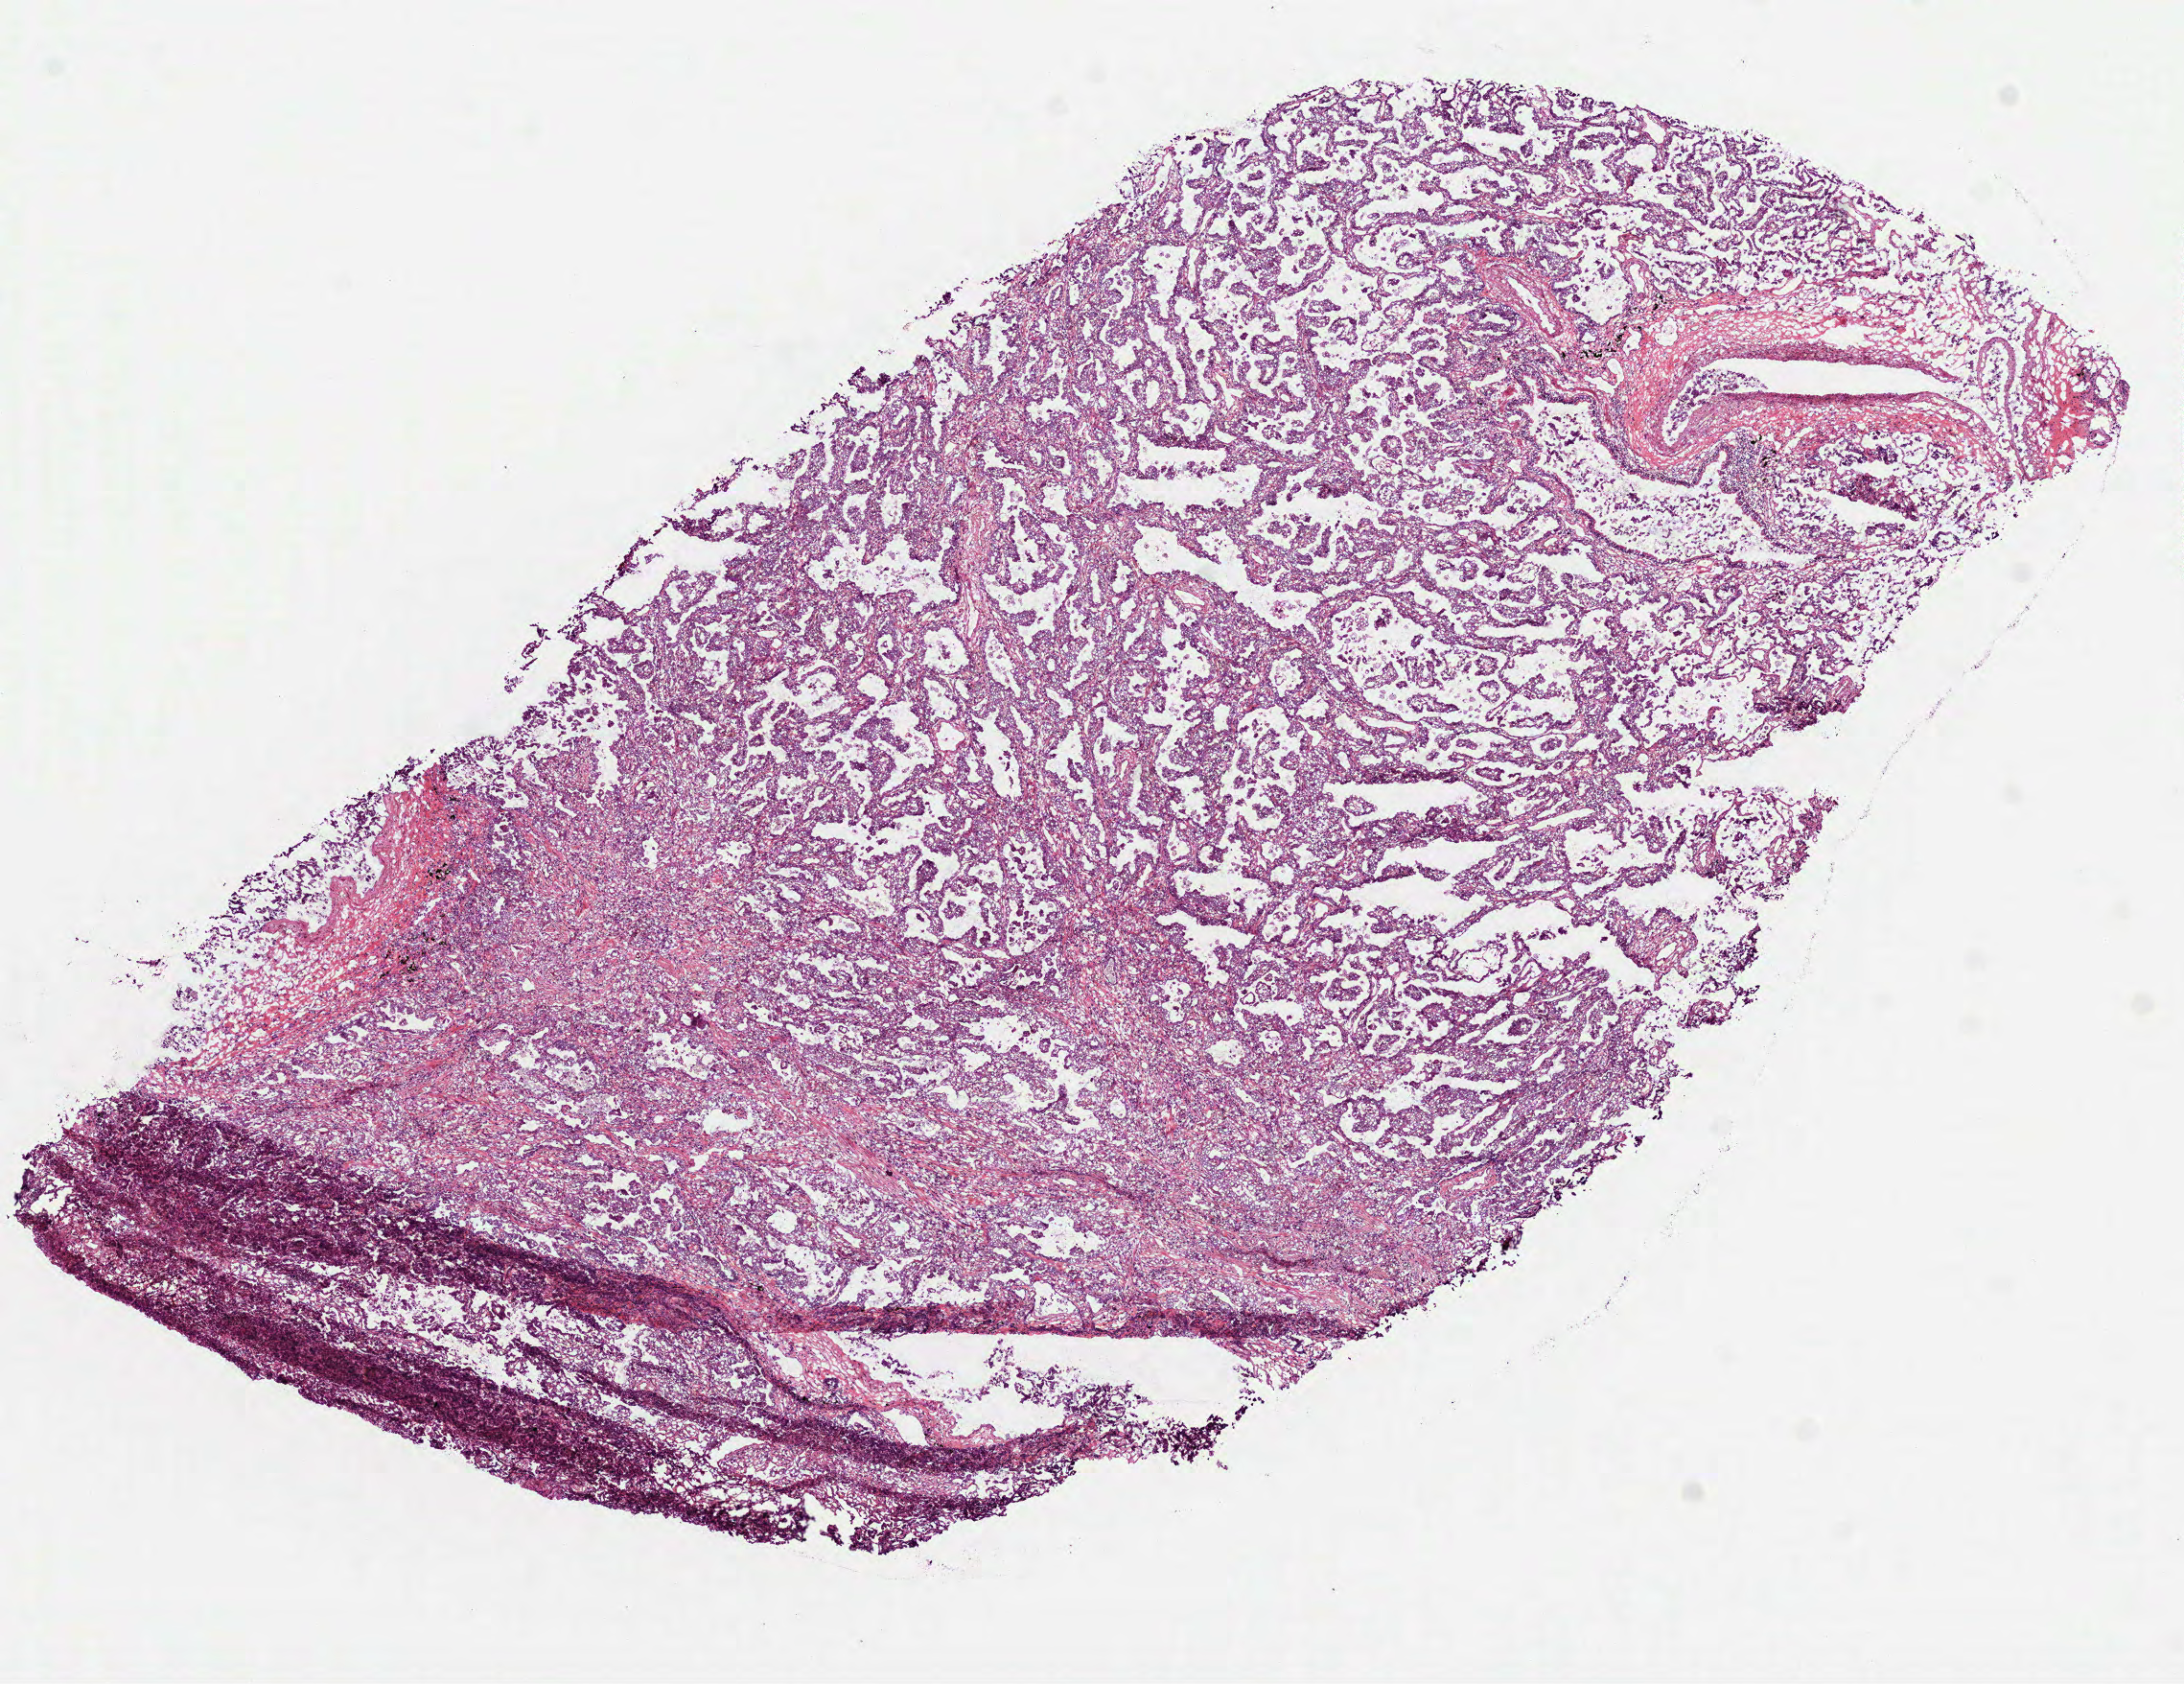
Digitized H&E-stained tissue section (whole slide) — low-resolution overview of the scanned area, about 9.2 x 7.1 mm (from a 40x scan), frozen section, sample: primary tumour, lung. Male patient; age at initial diagnosis 71 years. Composition of this section per pathologist review: tumour cells 80%, tumour nuclei 75%, normal cells 0%, stromal cells 15%, necrosis 5%.
Diagnosis: Adenocarcinoma with mixed subtypes (lower lobe, lung). AJCC pathologic stage: IIIB (6th edition). TNM: T4 N0 M0.